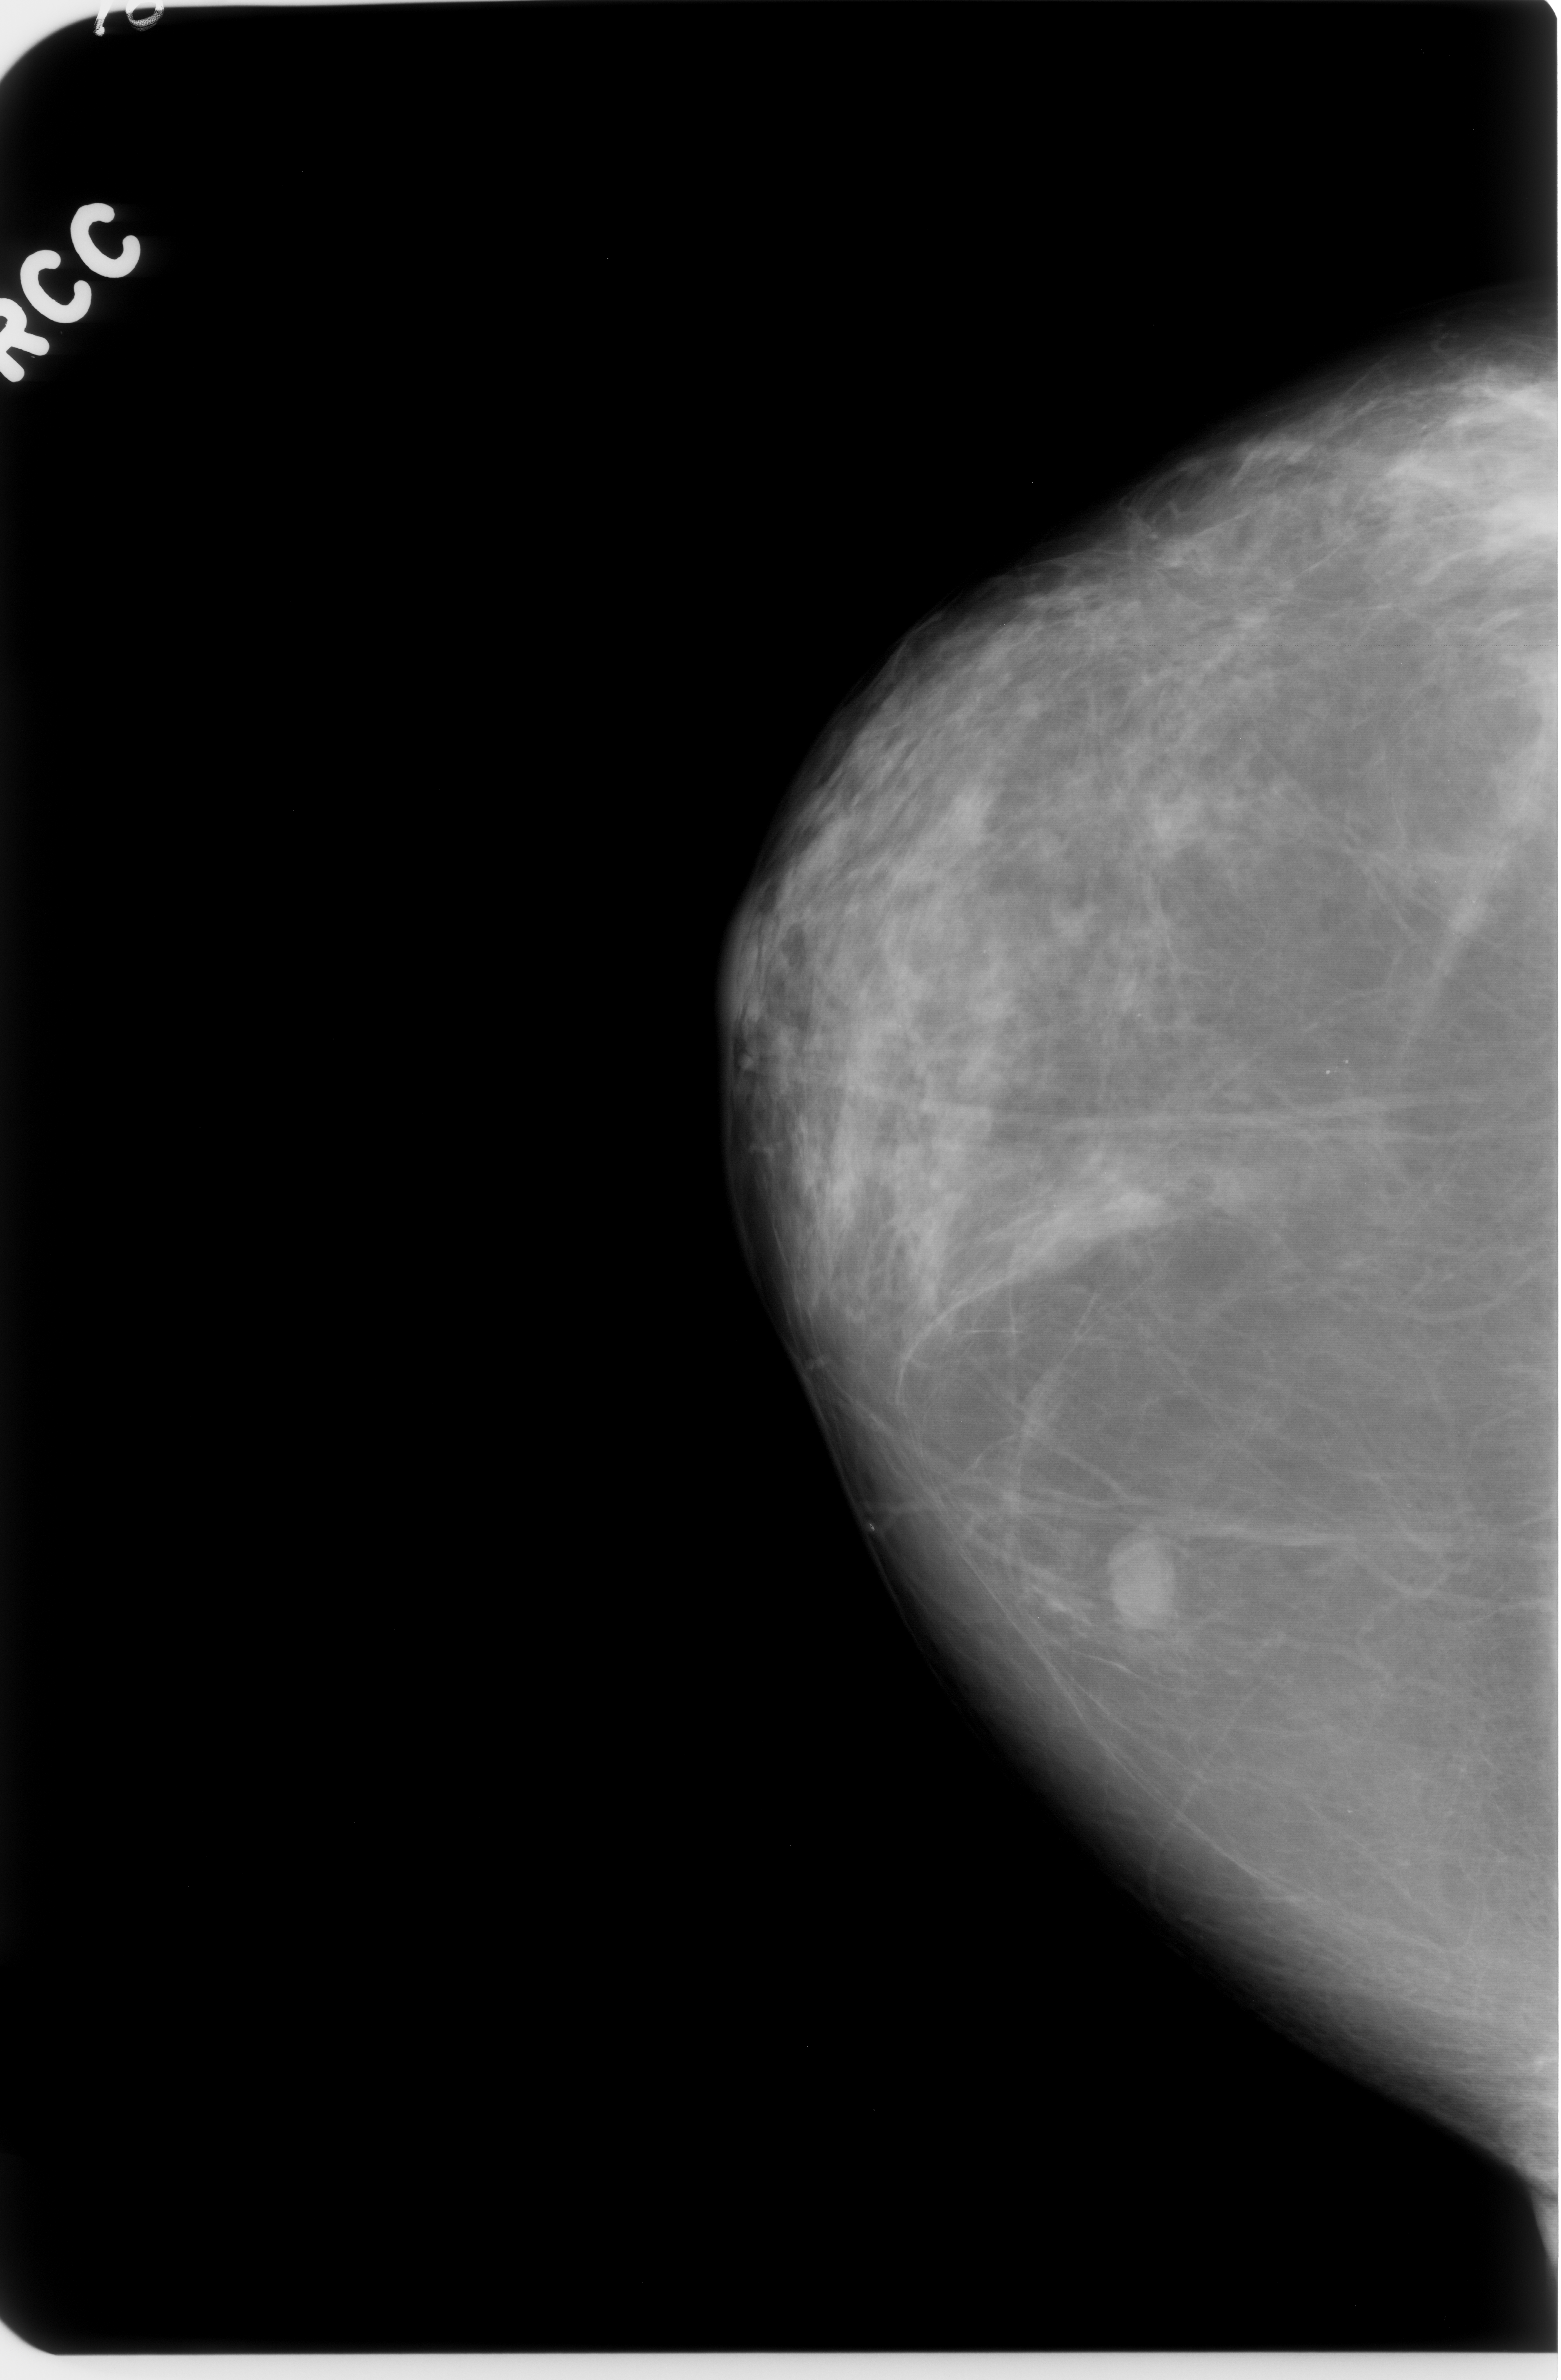
Digitized screen-film mammogram. Right breast. Craniocaudal (CC) view. 1561 × 2380 image matrix.
Expert-marked regions of interest on this film, with their recorded descriptors:
- mass, shape oval, margins circumscribed; BI-RADS assessment category 4; subtlety rating 5 on a 1 (subtle) to 5 (obvious) scale; pathology result (as recorded, not read from the image): benign: bounding box [x1, y1, x2, y2] px = [1101, 1534, 1181, 1649]